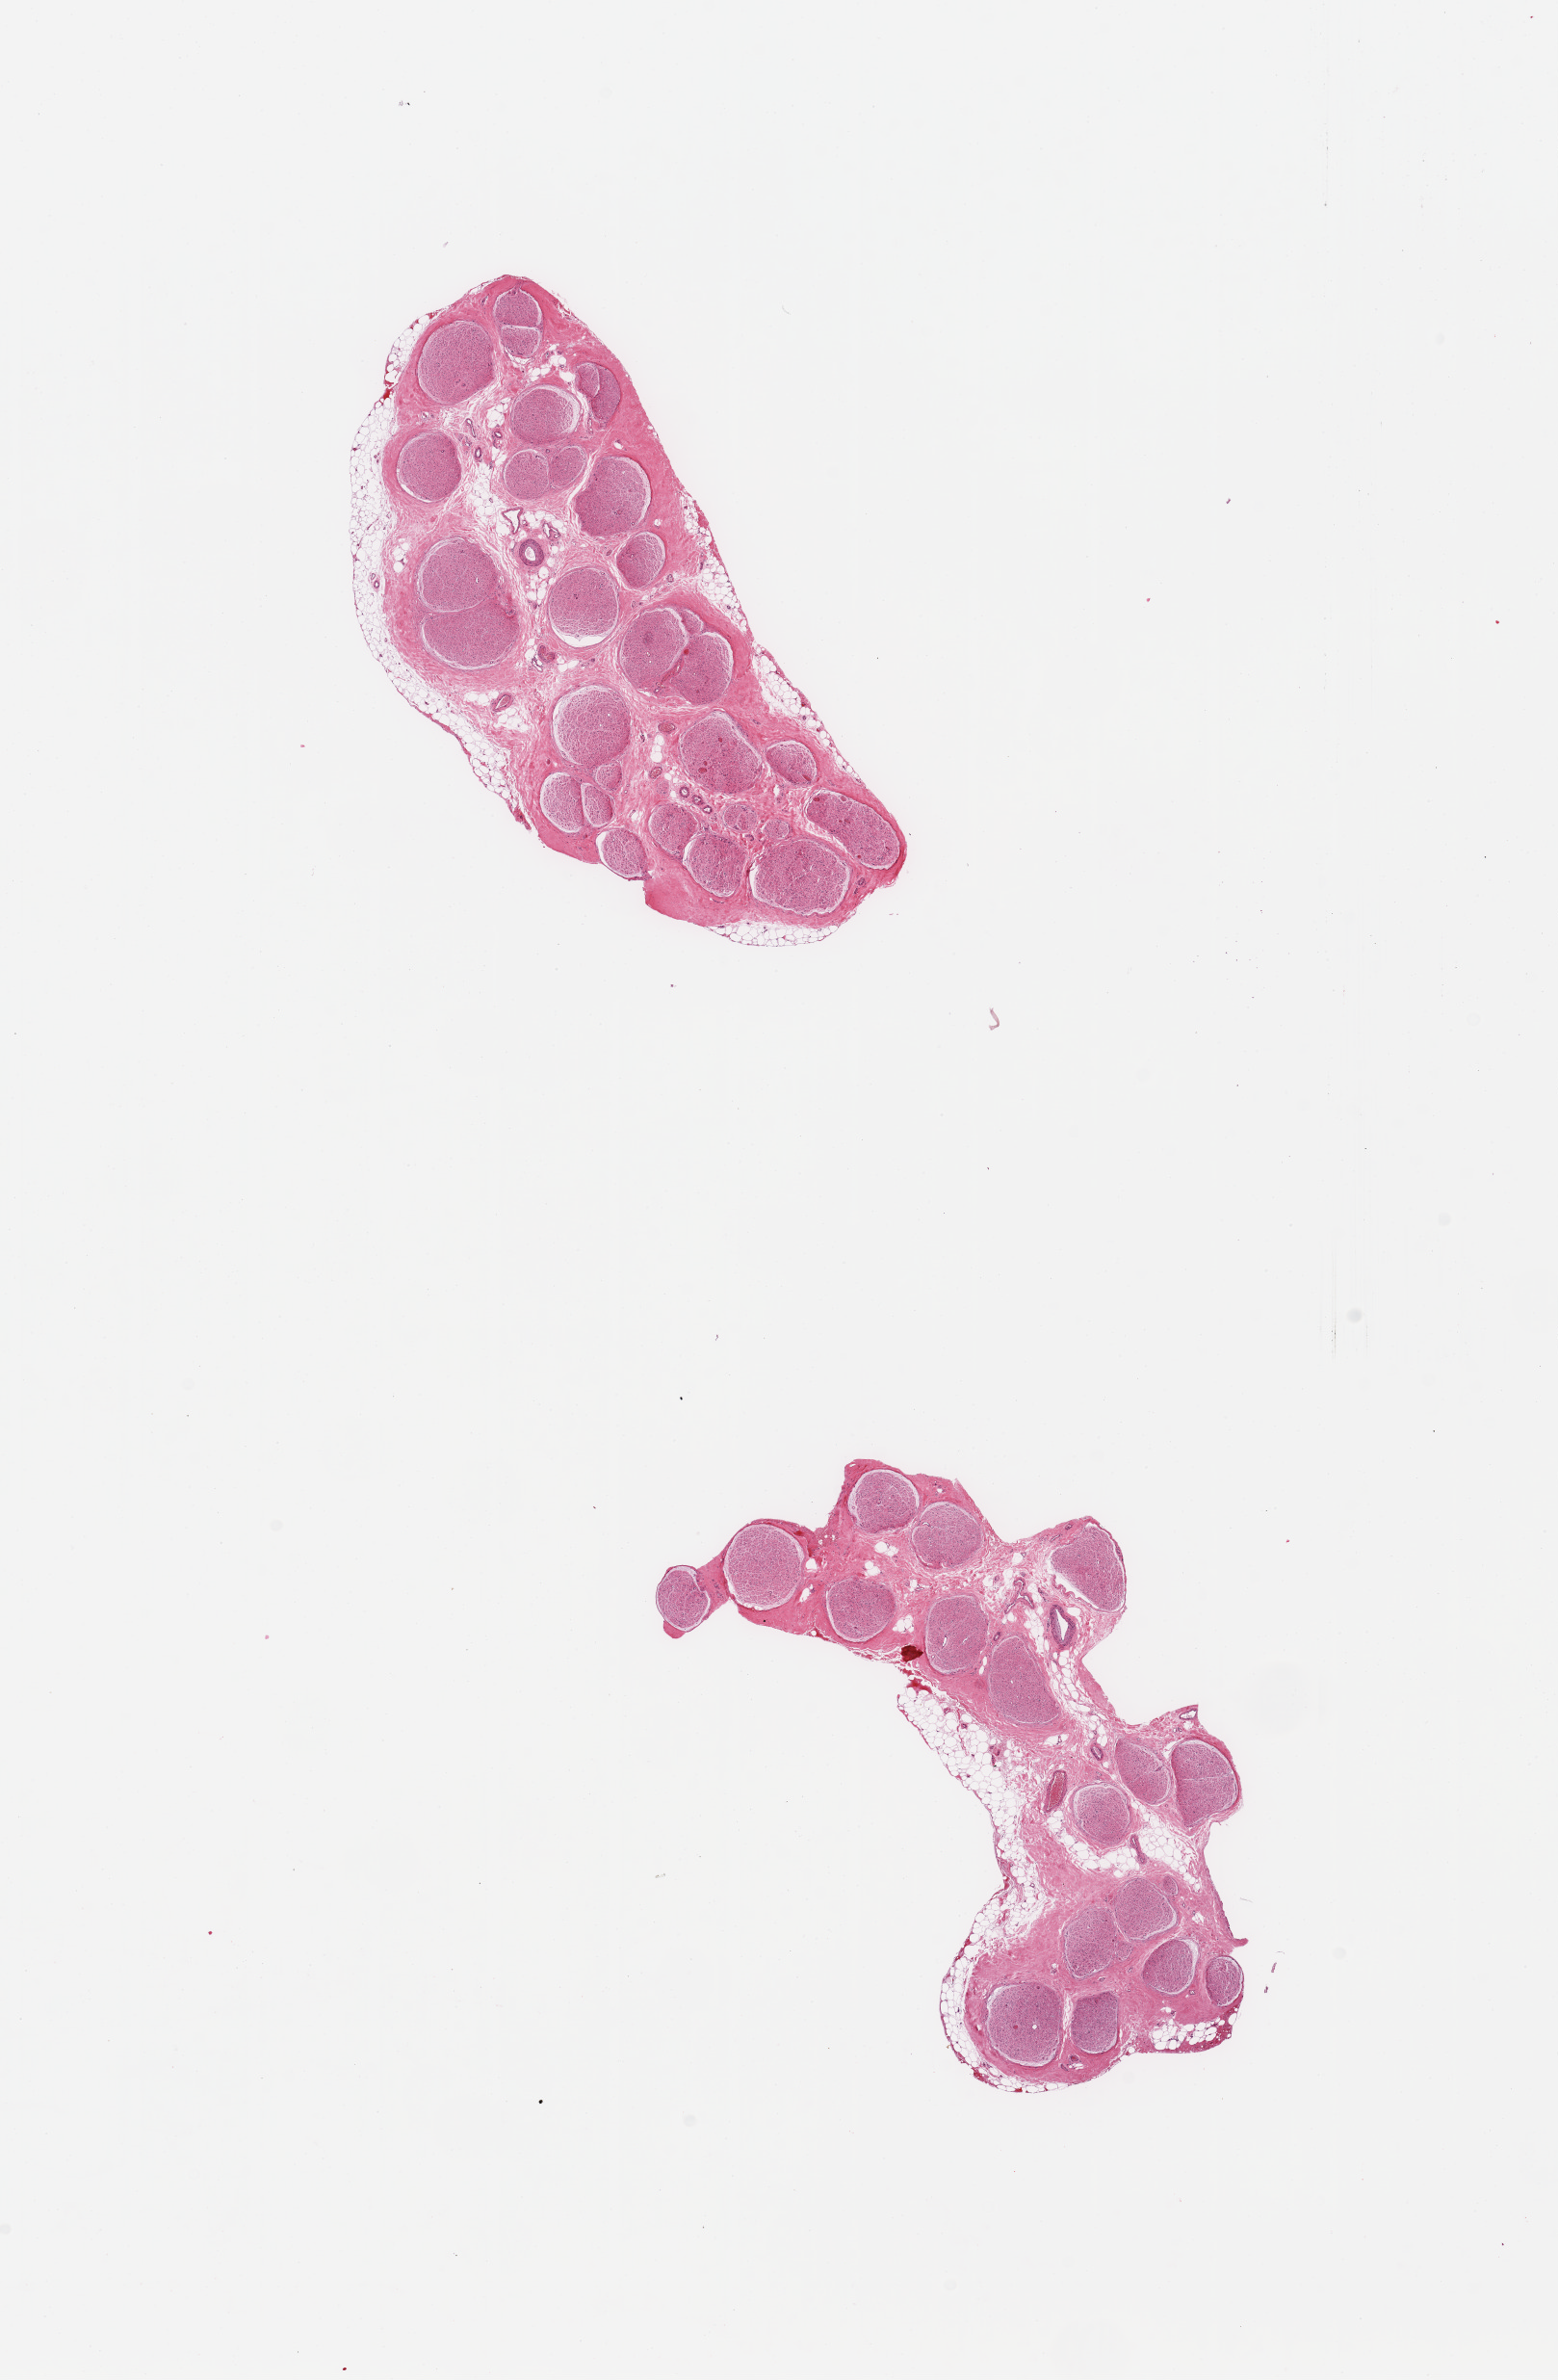
Haematoxylin and eosin whole-slide image, a low-resolution overview of the entire scanned area, about 12.8 x 19.5 mm (from a 20x scan). PAXgene-fixed paraffin-embedded (PFPE) section. Target tissue: tibial nerve. Donor tissue sample.
- reviewer comment on this tissue sample: 2 pieces; 10% internal & external fat